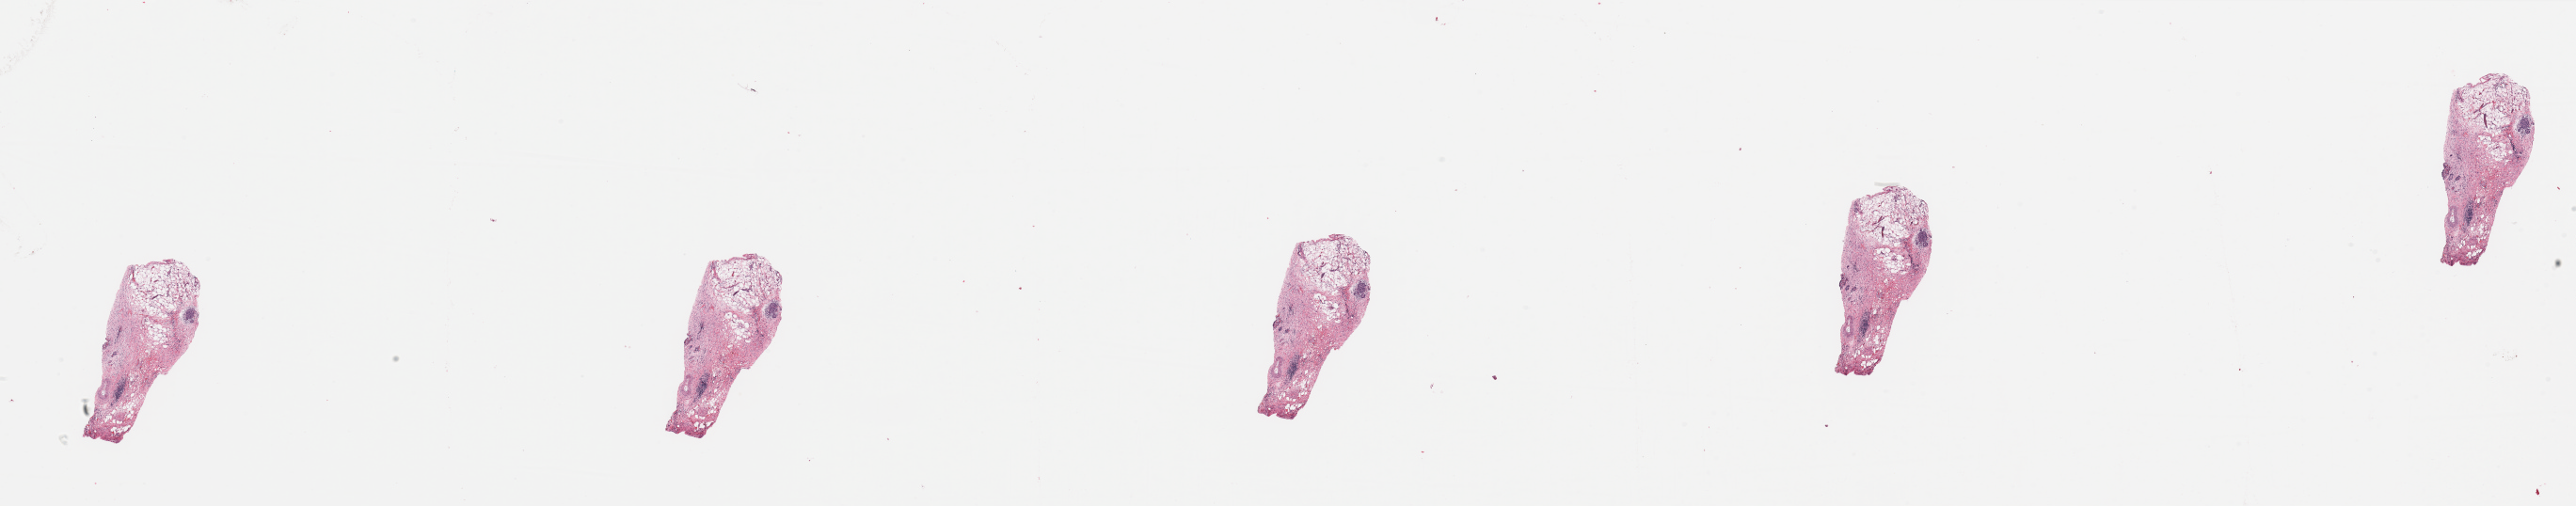
Whole-slide histology image, H&E-stained — shown as a low-resolution overview of the whole scanned area (about 43.3 x 8.5 mm), pancreas, tumour tissue. 75-year-old male patient.
• patient diagnosis (cohort enrolment): ductal adenocarcinoma (pancreas)